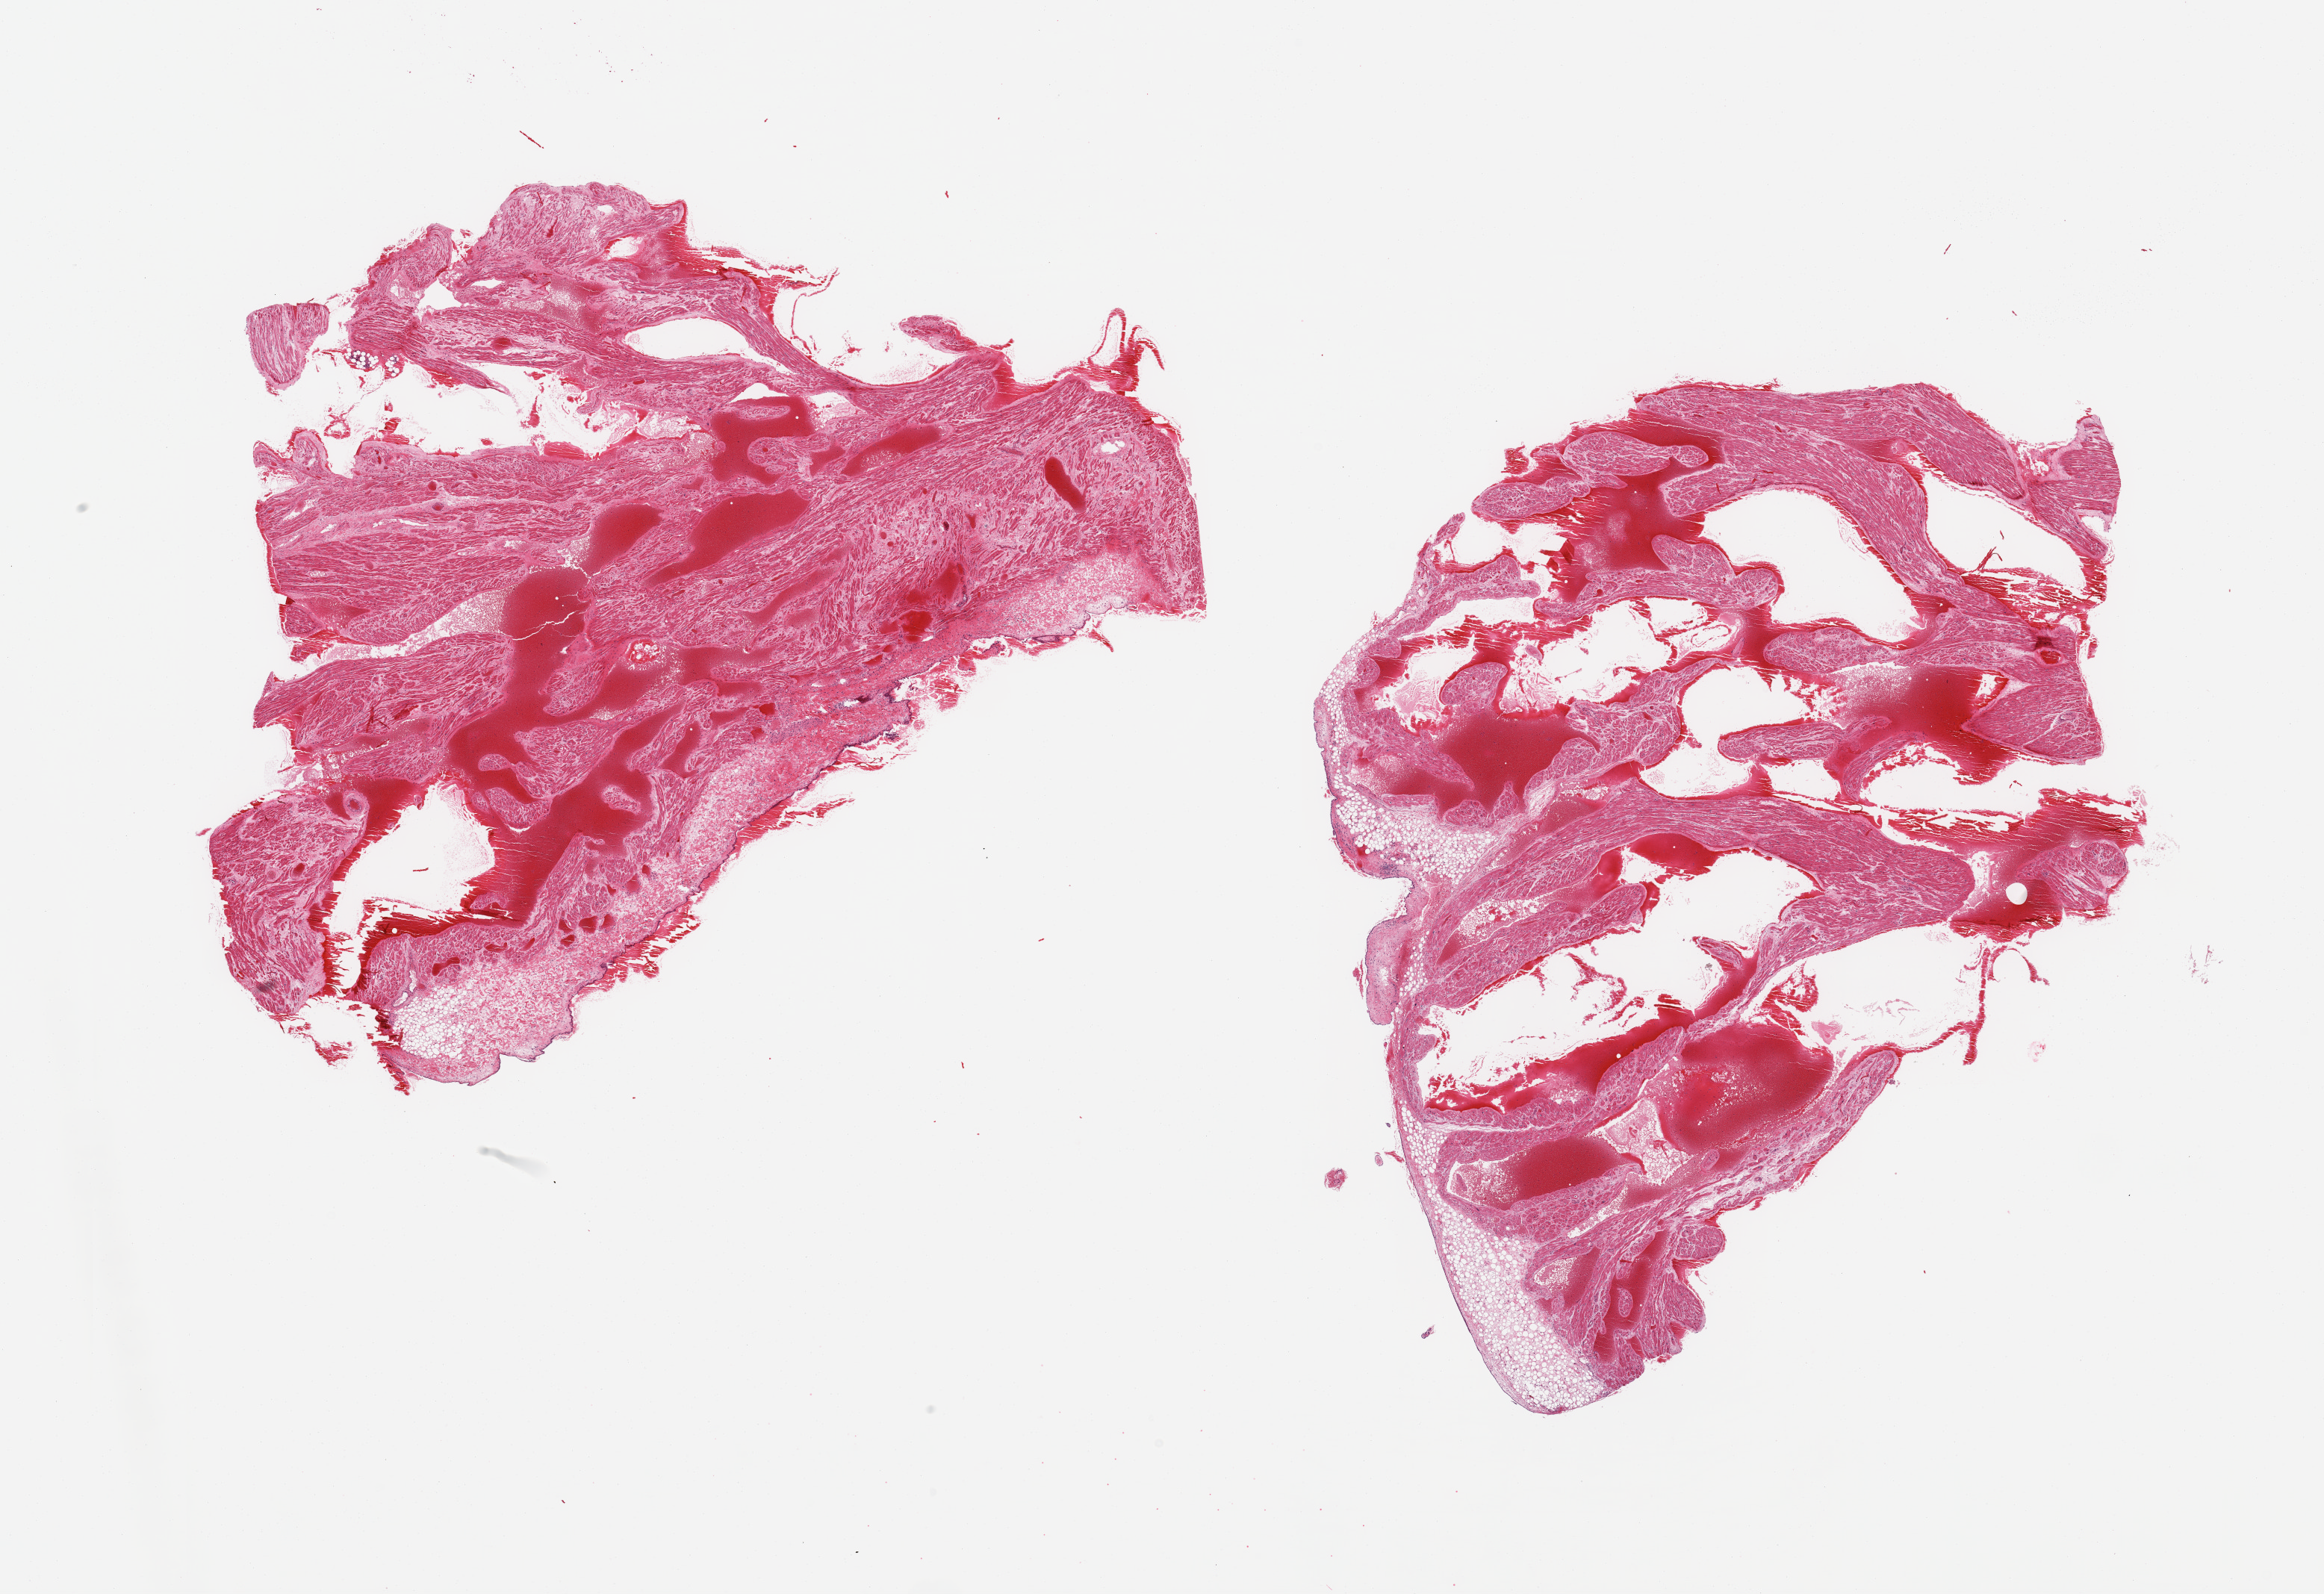
Whole-slide image, hematoxylin and eosin (H&E) stain, low-resolution overview of the scanned area, about 24.6 x 16.9 mm (slide scanned at 20x); PAXgene-fixed, paraffin-embedded tissue; target tissue: auricular appendage; tissue donor sample.
Reviewer comment on this tissue sample: 2 pieces; fibromuscular and adipose tissue; marked congestion with stasis.